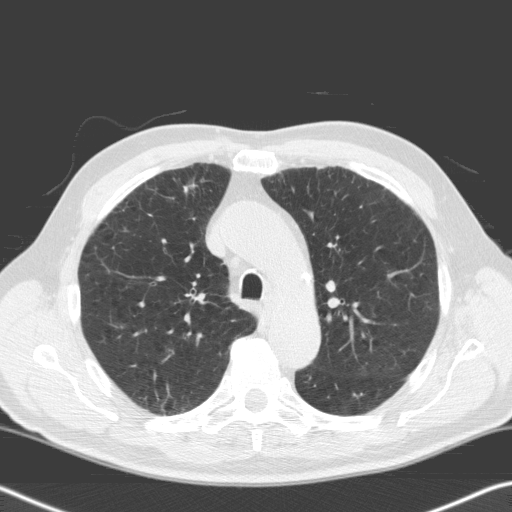
Low-dose screening chest CT, axial slice. Baseline annual screen. Lung window (W 1500 / L -600 HU). Slice 46 of 170 in the series. 512 × 512 image matrix, field of view 343 × 343 mm. Male participant, aged 68 years at enrolment. Current smoker at enrolment.
Expert reader's lesion annotation, box from (x=158, y=167) to (x=208, y=216) px. The exam's reader record, not a measurement of the box and not confirmed to be the same lesion: non-calcified nodule or mass ≥4 mm, right upper lobe, 18 × 12 mm, spiculated (stellate) margins, soft tissue attenuation. Participant outcome: lung cancer diagnosed 73 days after this screen — squamous cell carcinoma, NOS, right upper lobe, moderately differentiated (G2), stage IIIA (AJCC 6th edition), 7 mm at pathology.